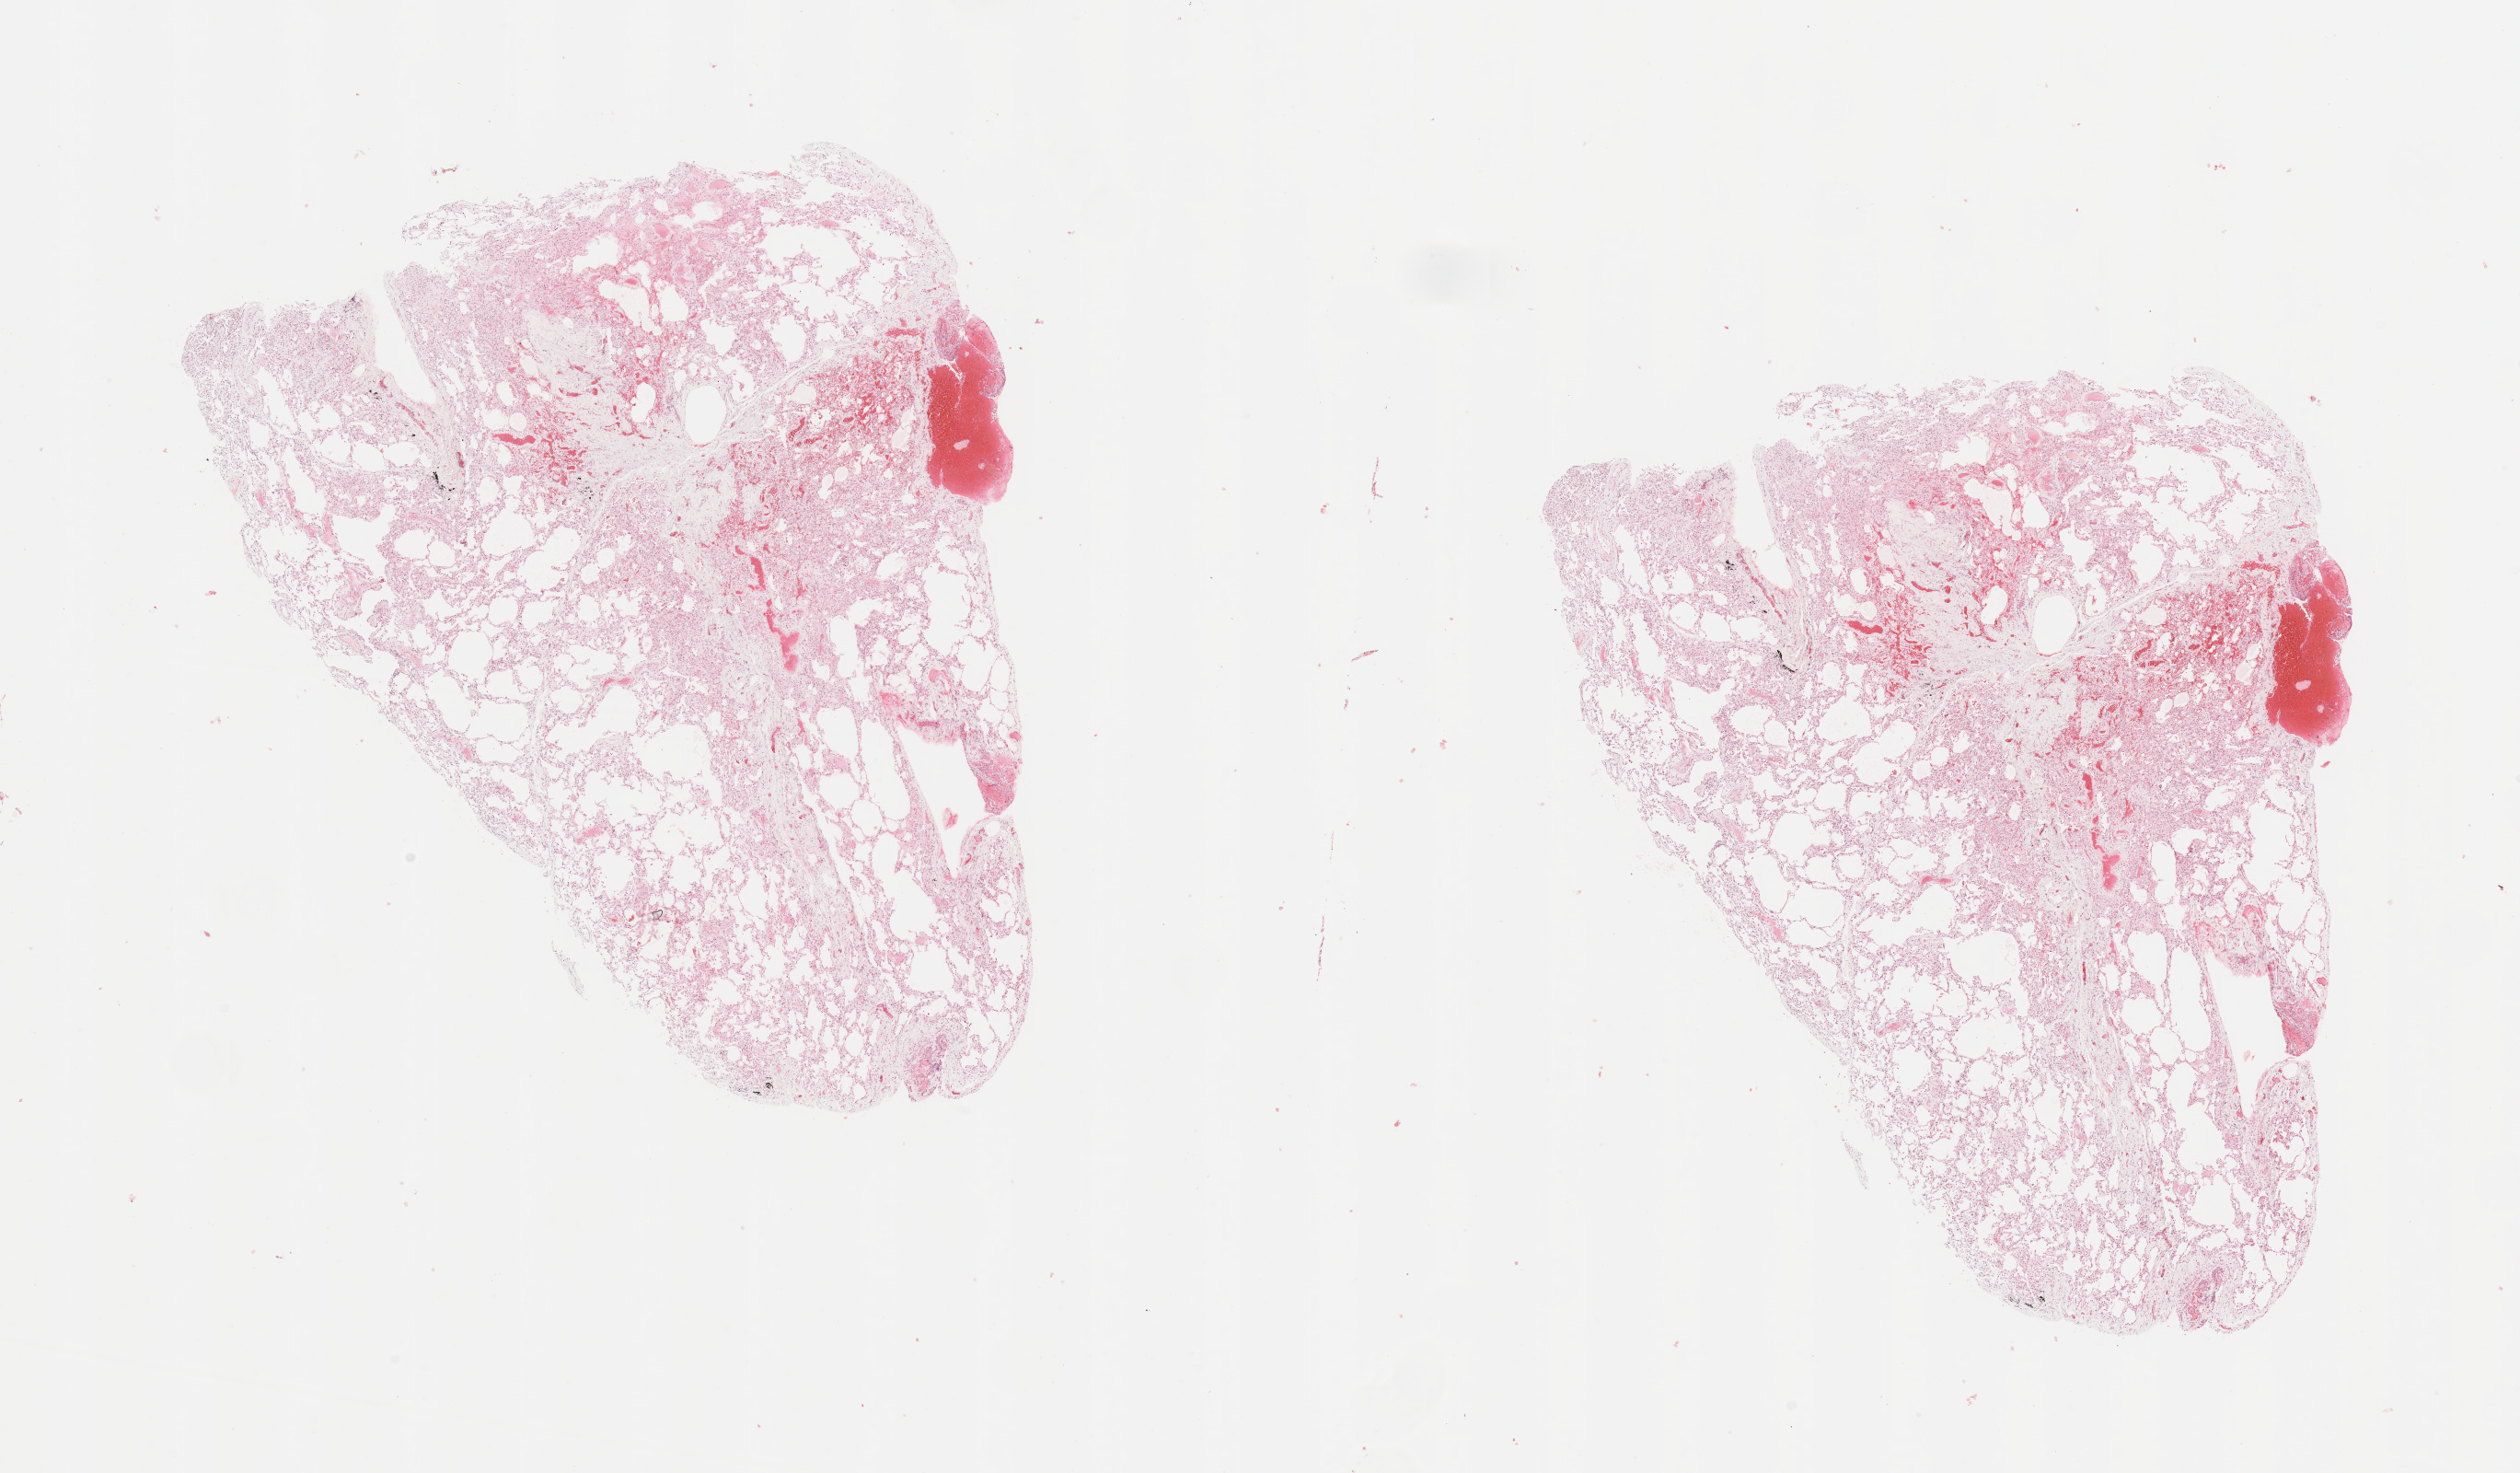
Digitized H&E tissue section (whole slide), a low-resolution overview of the entire scanned area, about 21.7 x 12.7 mm (acquisition: 20x scan). Normal (non-tumour) tissue sample, lung. Female, 66 y/o.
This section: normal (non-tumour) tissue from the same patient. Patient diagnosis: Squamous cell carcinoma, NOS.